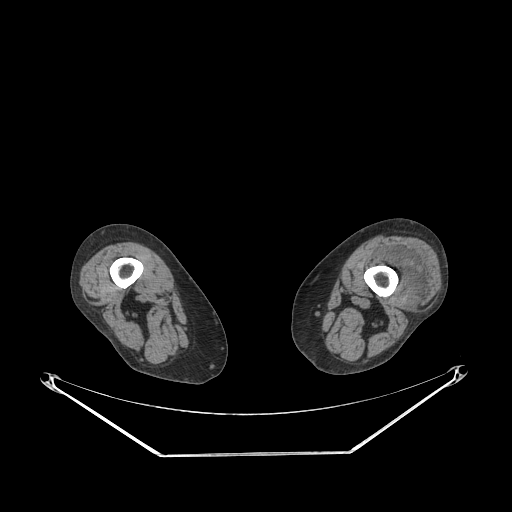
CT of an extremity soft-tissue mass (from a PET/CT study), one axial slice. Slice 197 of 267 in the series (ordered by position). 140 kVp. Soft-tissue window (W 400 / L 40 HU). 512 × 512 image matrix, field of view 500 × 500 mm. Female patient. From the clinical record (not read from this slice): histological type: undifferentiated – high grade; grade: high; site of the primary tumour: left thigh.
Outlined on this slice (expert contour drawn on MRI and transferred to this co-registered scan by the dataset authors):
- gross tumour volume including surrounding oedema: bounding box (x1, y1, x2, y2) in pixels: (372, 247, 430, 298)